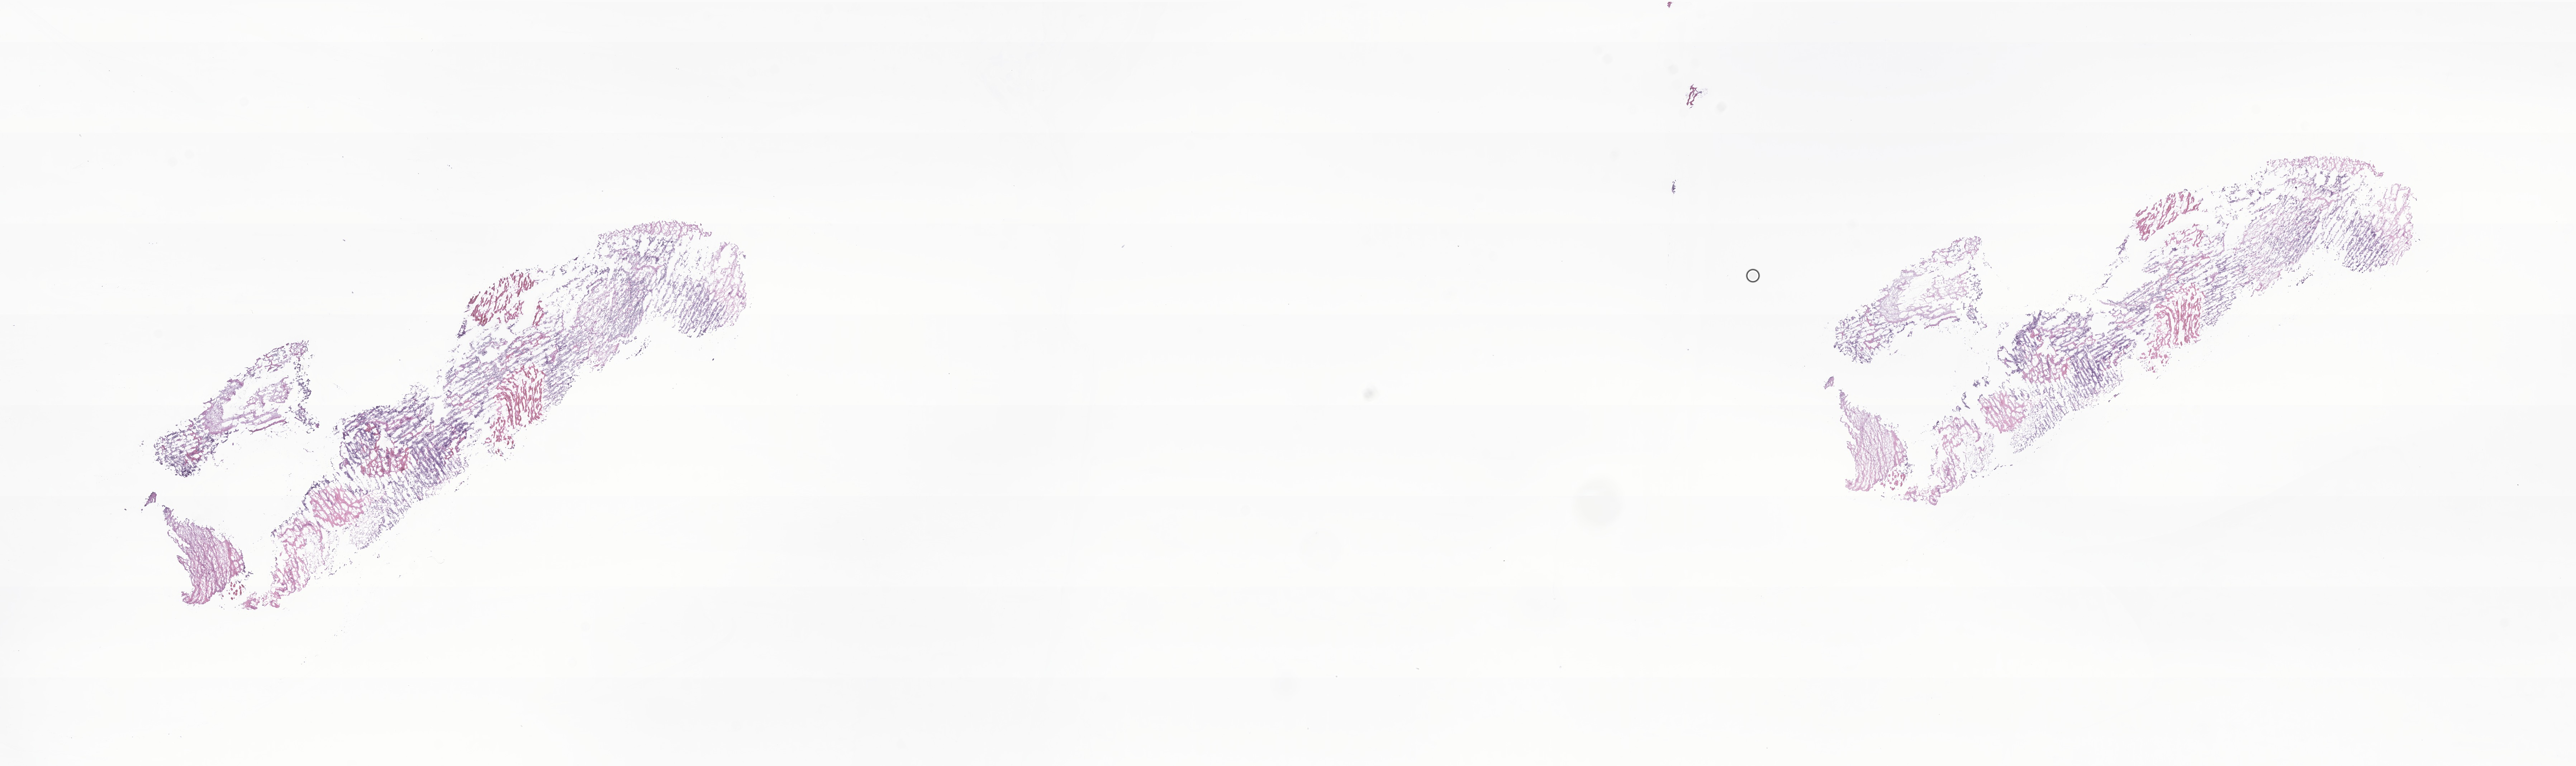
Digitized haematoxylin and eosin-stained section of tumor tissue from the kidney, shown as a low-resolution overview of the whole scanned area (about 30.3 x 9.0 mm). Frozen section. Patient female; age 803 days (about 2.2 years).
• diagnosis (ICD-O-3 morphology term): Neuroblastoma, NOS